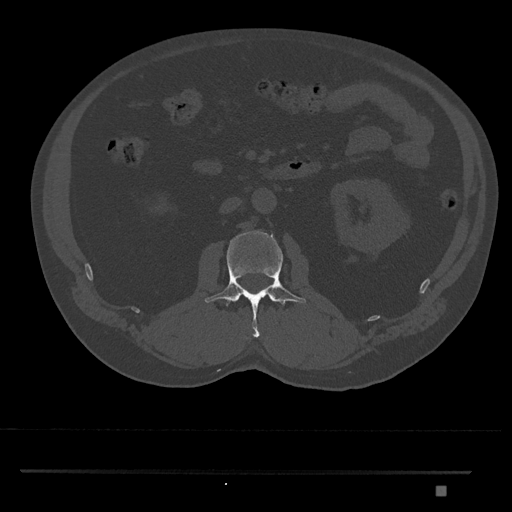
CT including the spine, one axial slice; reconstruction kernel Br40s/3; 120 kVp; bone window (W 1800 / L 400 HU); 0.5 mm slice thickness; 512 × 512 image matrix. Patient: male, 65 years. Case-level facts recorded for this patient, not image findings: primary cancer: prostate.
Outlined on this slice (semi-automatically segmented with operator editing):
- L2 vertebra: bounding box <204,230,307,338> (left, top, right, bottom; pixels)